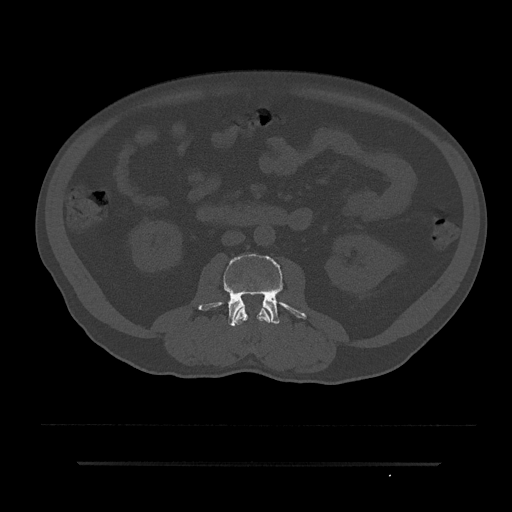
CT including the spine, one axial slice. Slice 26 of 797 in the series (ordered by position). Reconstruction kernel Br40s/3. Bone window (W 1800 / L 400 HU). 512 × 512 image matrix, field of view 464 × 464 mm. Patient: male, 59 years. Case-level facts recorded for this patient, not image findings: primary cancer: bile ducts; vertebrae with lytic lesions (as recorded): T10.
Annotated regions visible in this slice (semi-automatic segmentation, software-assisted and operator-edited):
- L2 vertebra: box from (x=233, y=305) to (x=273, y=325) px
- L3 vertebra: (x=199, y=253)–(x=306, y=326)